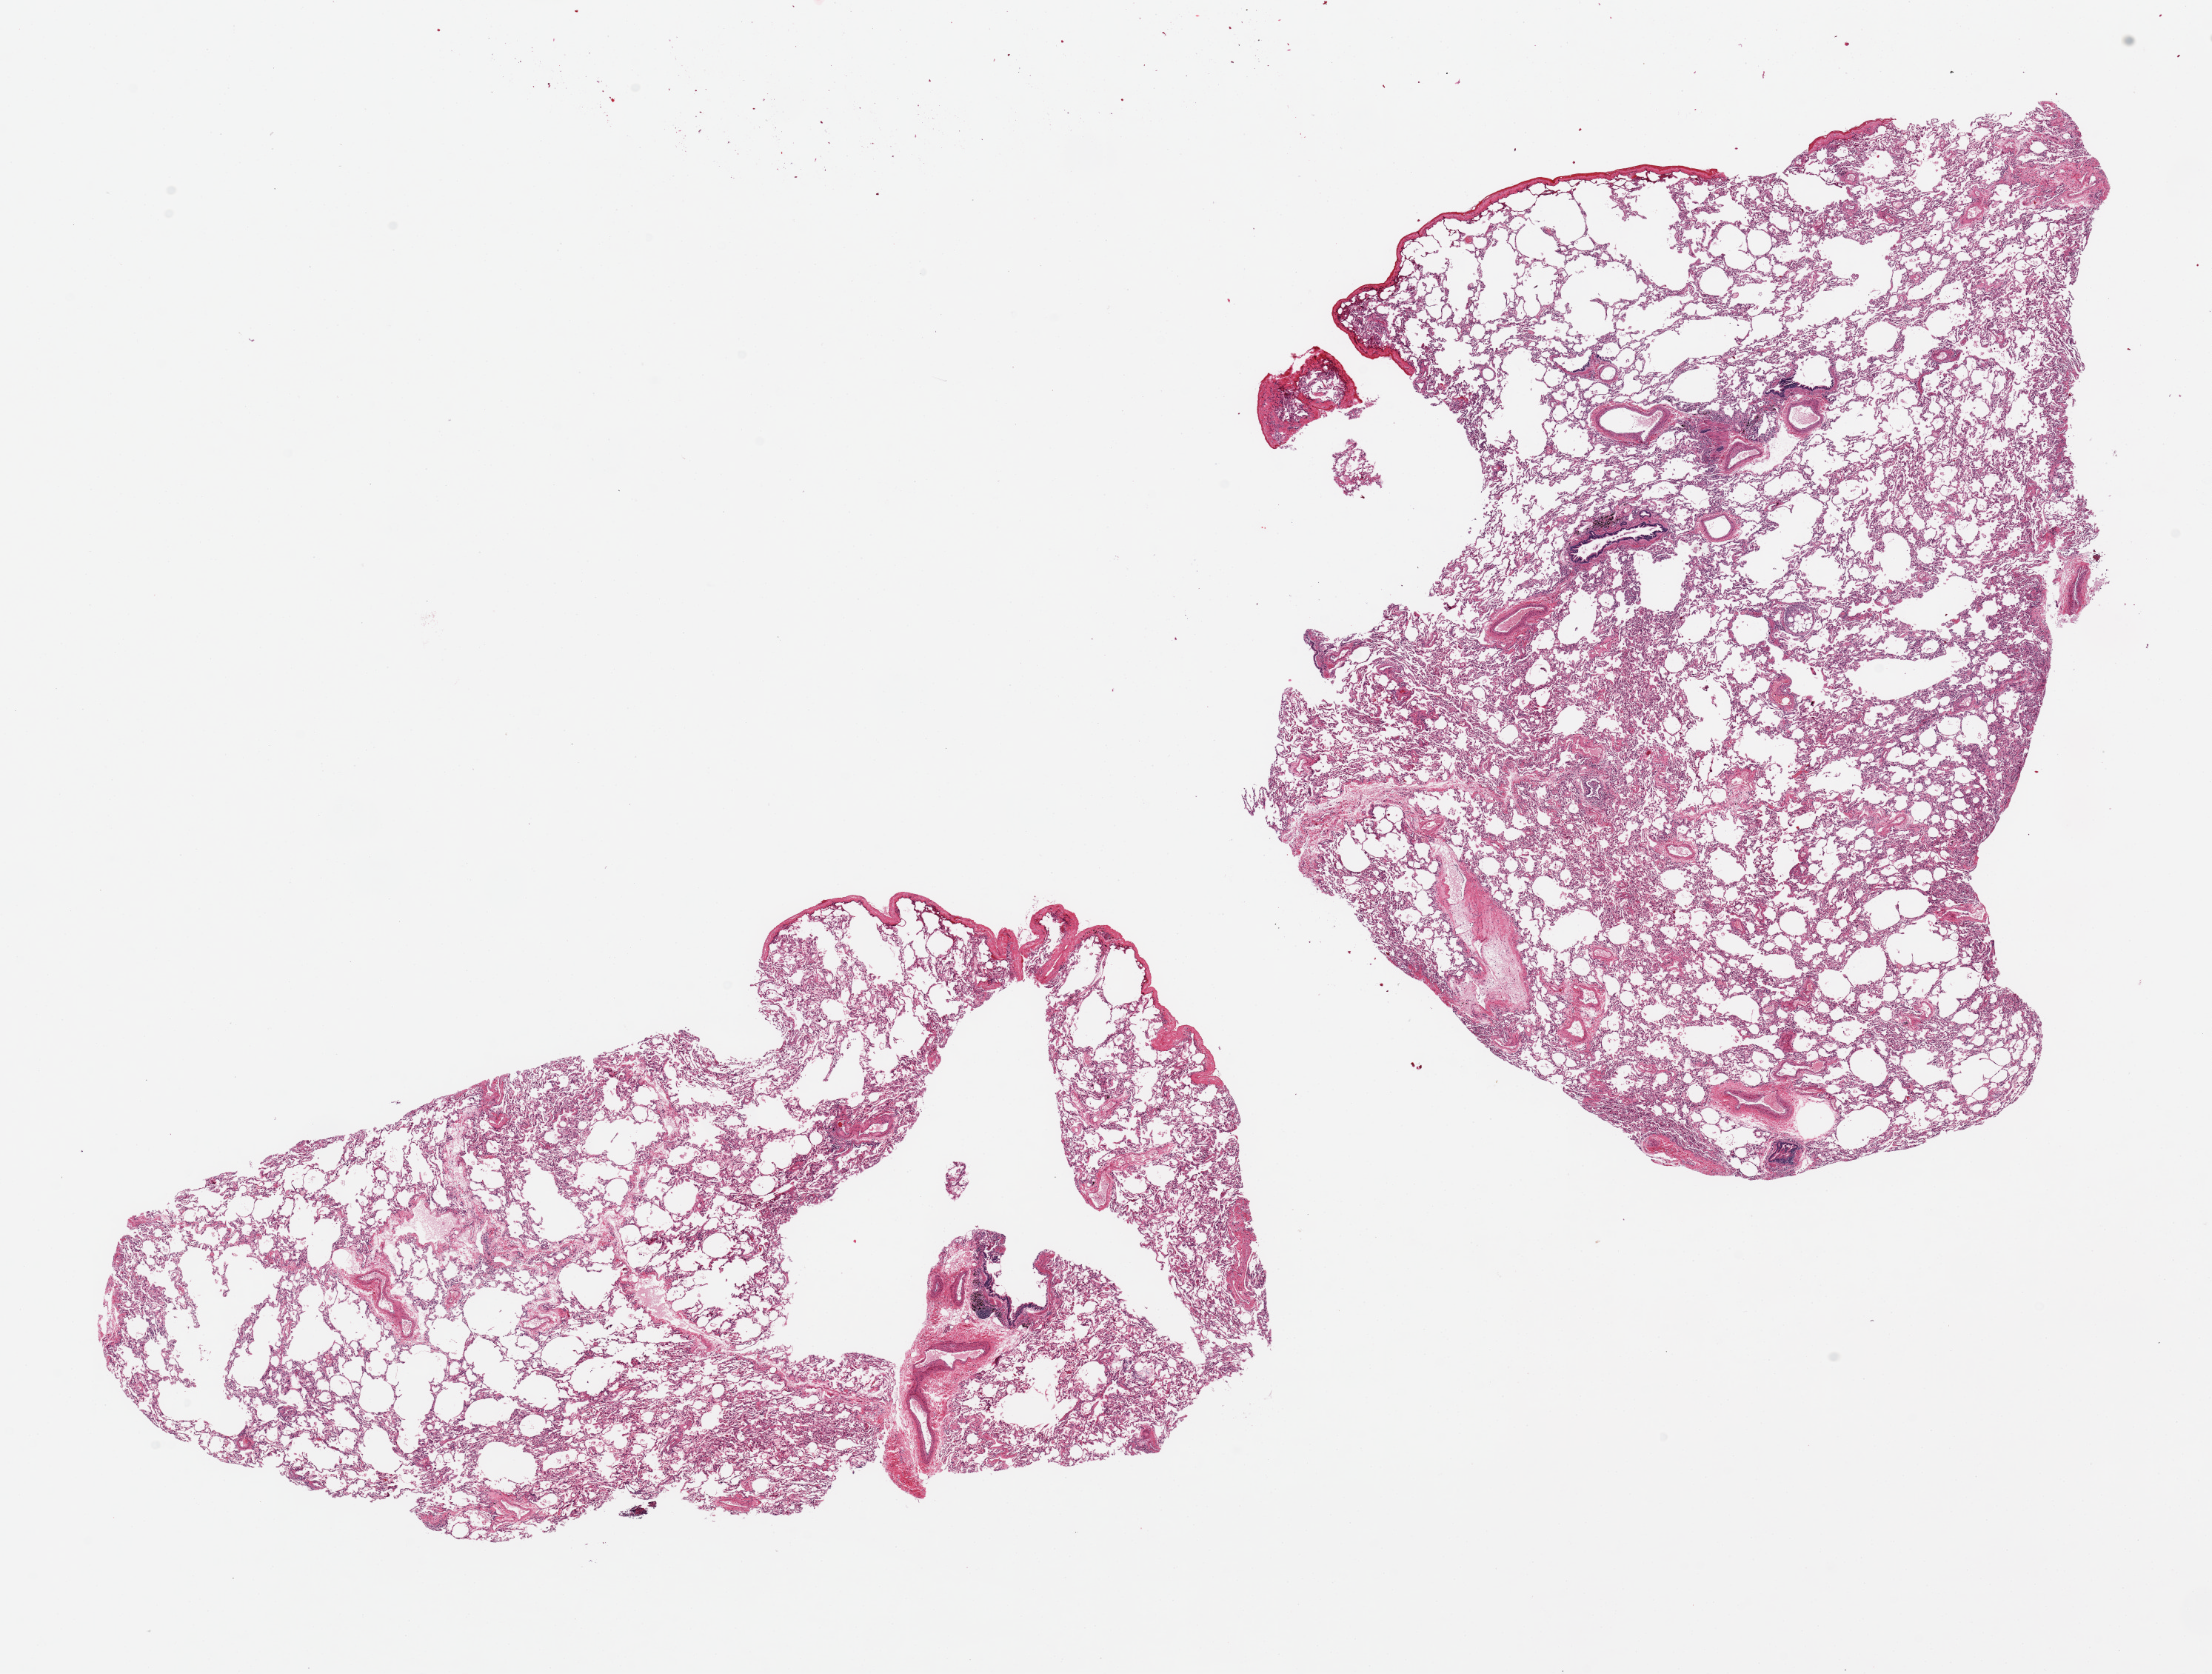
Haematoxylin and eosin whole-slide image, whole scanned area (about 23.6 x 17.9 mm, from a 20x scan) shown as a low-resolution overview; PAXgene-fixed, paraffin-embedded tissue; sampled site (target tissue): lung; donor tissue sample.
• reviewer comment on this tissue sample: 2 pieces; include pleura (target is 1 cm below pleura), some widening of airspaces, small bone marrow embolism